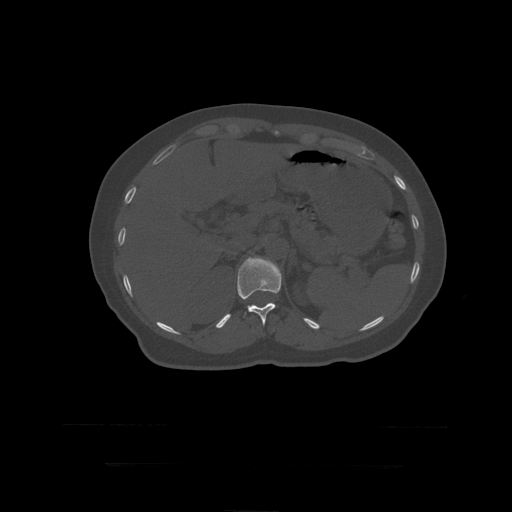
CT including the spine, one axial slice; position 195 of 399 along the scan axis; 120 kVp; bone window (W 1800 / L 400 HU); 512 × 512 image matrix, field of view 450 × 450 mm. Patient age 41 years. Case-level facts recorded for this patient, not image findings: primary cancer: breast.
Annotated regions visible in this slice (semi-automatic segmentation, software-assisted and operator-edited):
- T12 vertebra: bounding box (x1, y1, x2, y2) in pixels: (237, 256, 282, 326)